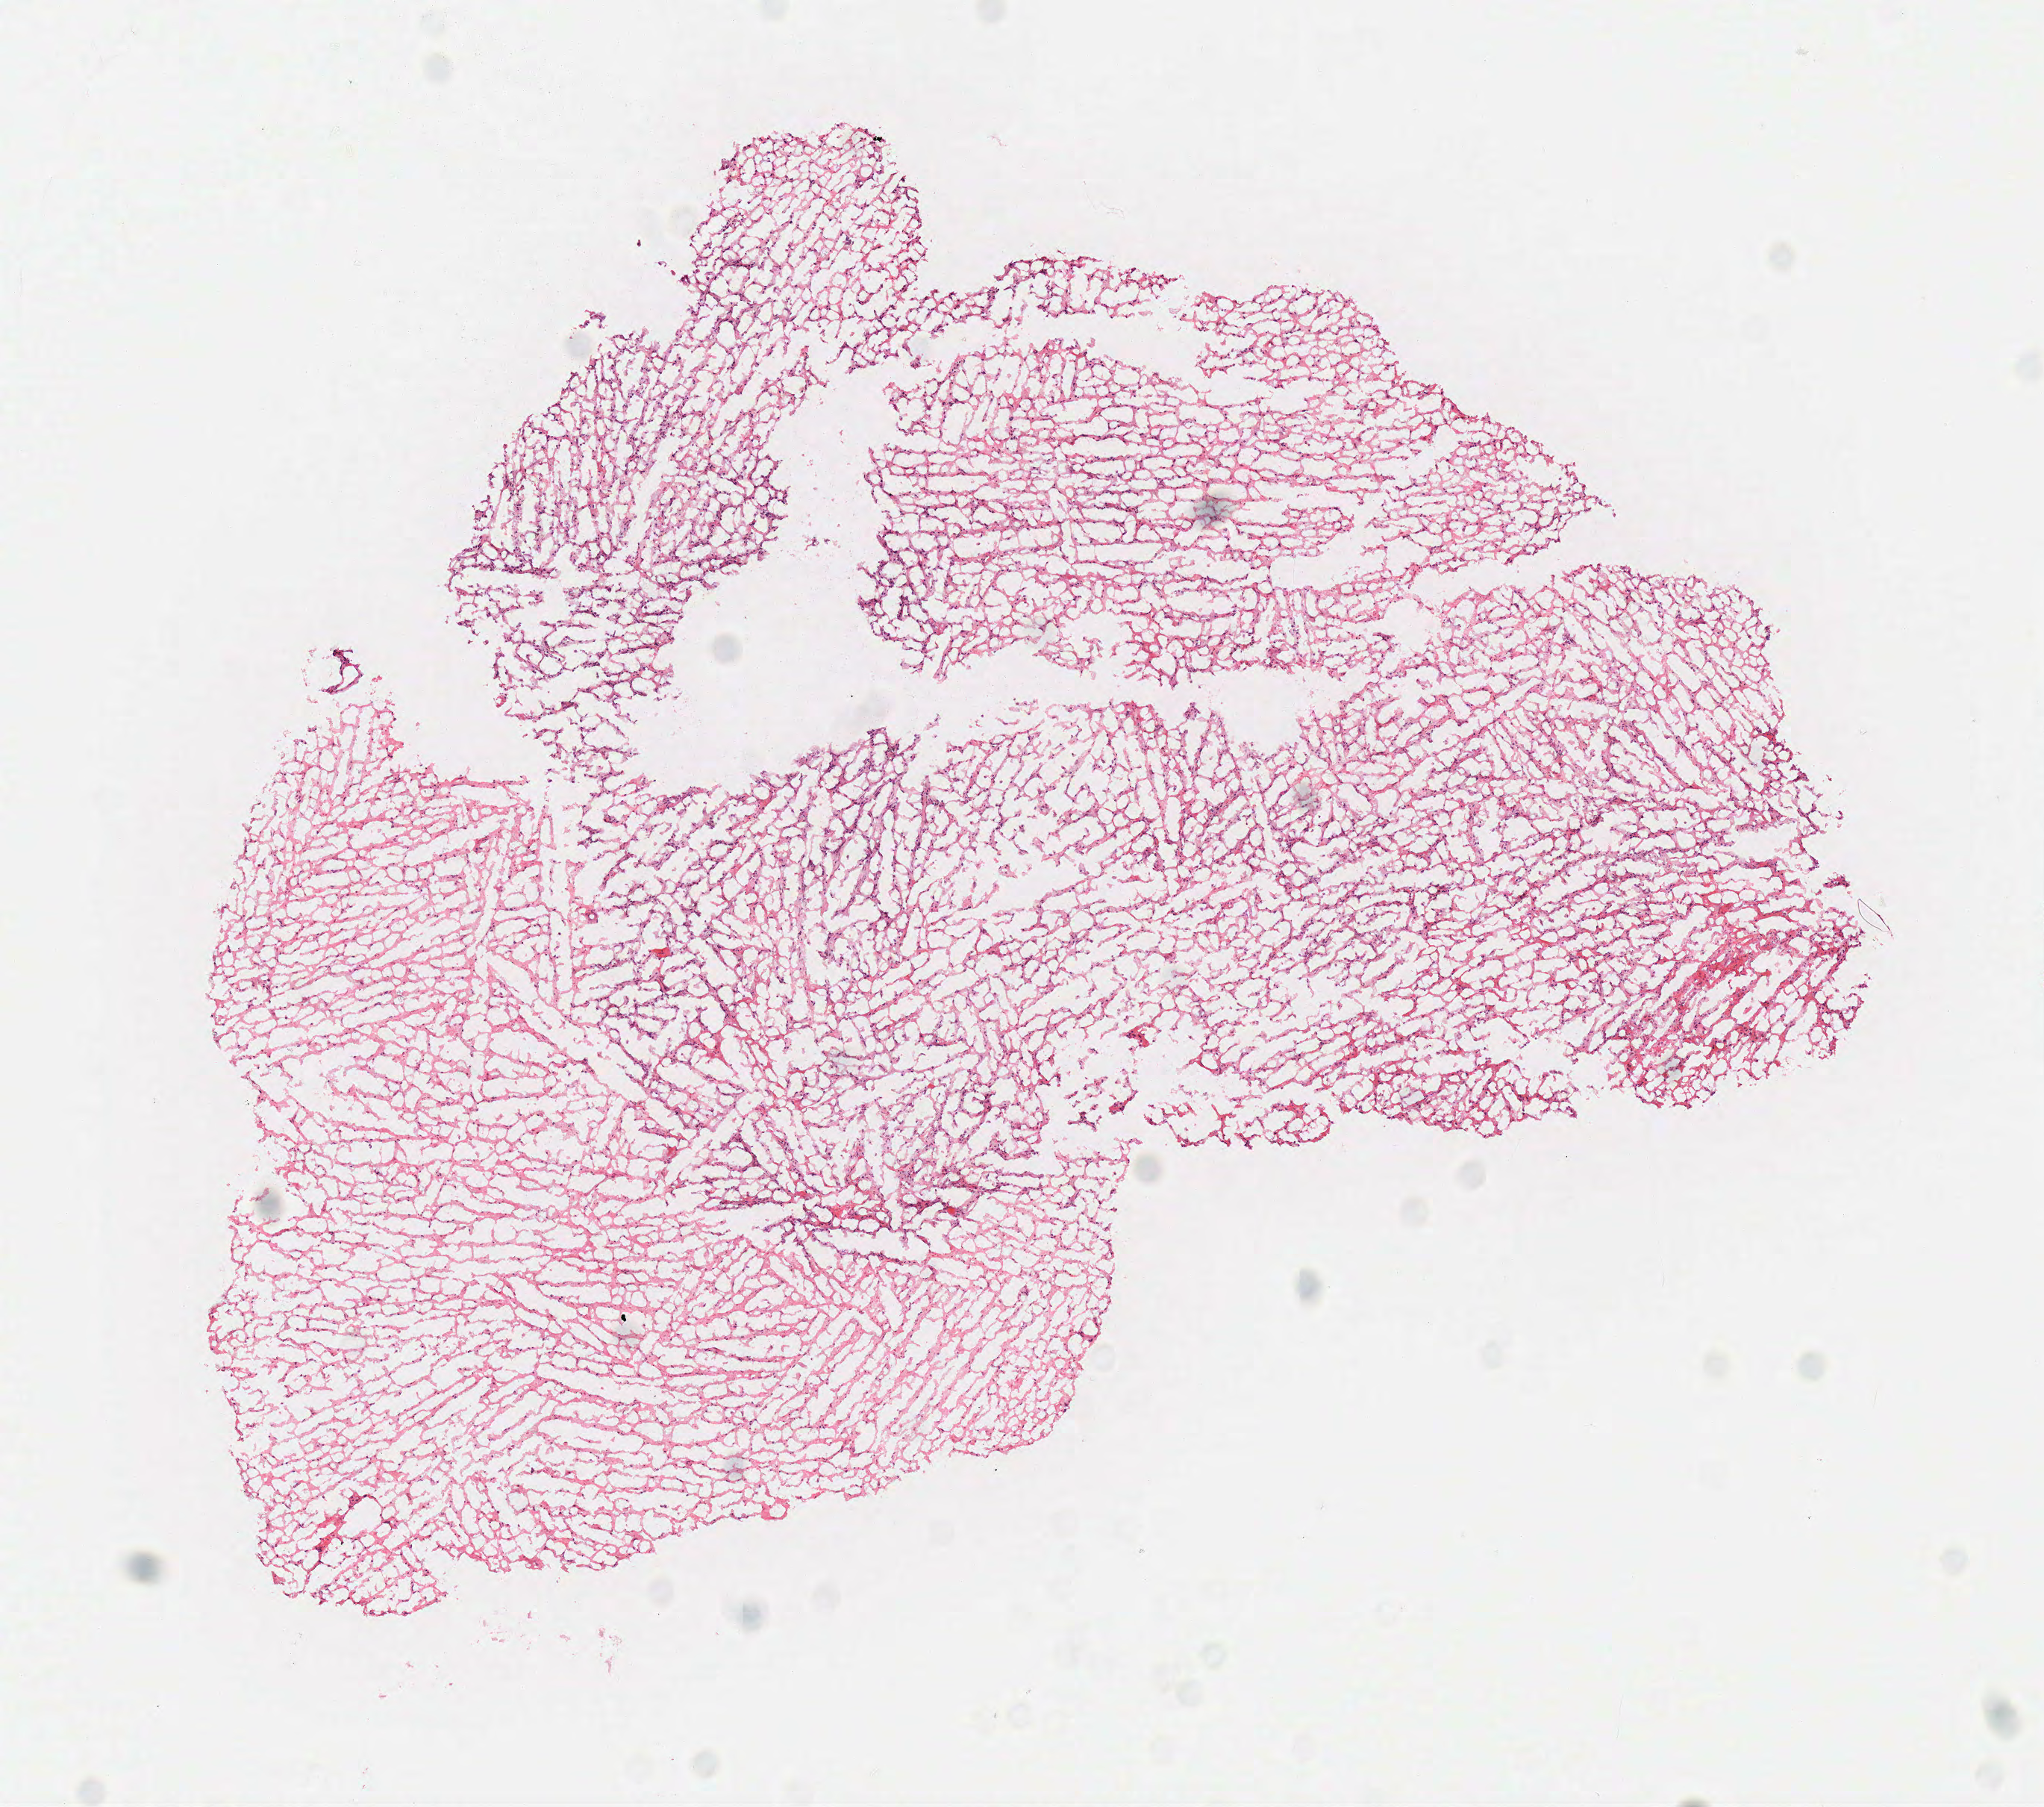
Digitized H&E tissue section (whole slide), whole scanned area (about 5.4 x 4.8 mm, acquisition: 40x scan) shown as a low-resolution overview; frozen section; brain, primary tumour sample. Male patient; age at initial diagnosis 83 years. Composition of this section per pathologist review: tumour cells 100%, tumour nuclei 60%, normal cells 0%, stromal cells 0%, necrosis 0%.
Histologic diagnosis: Glioblastoma.